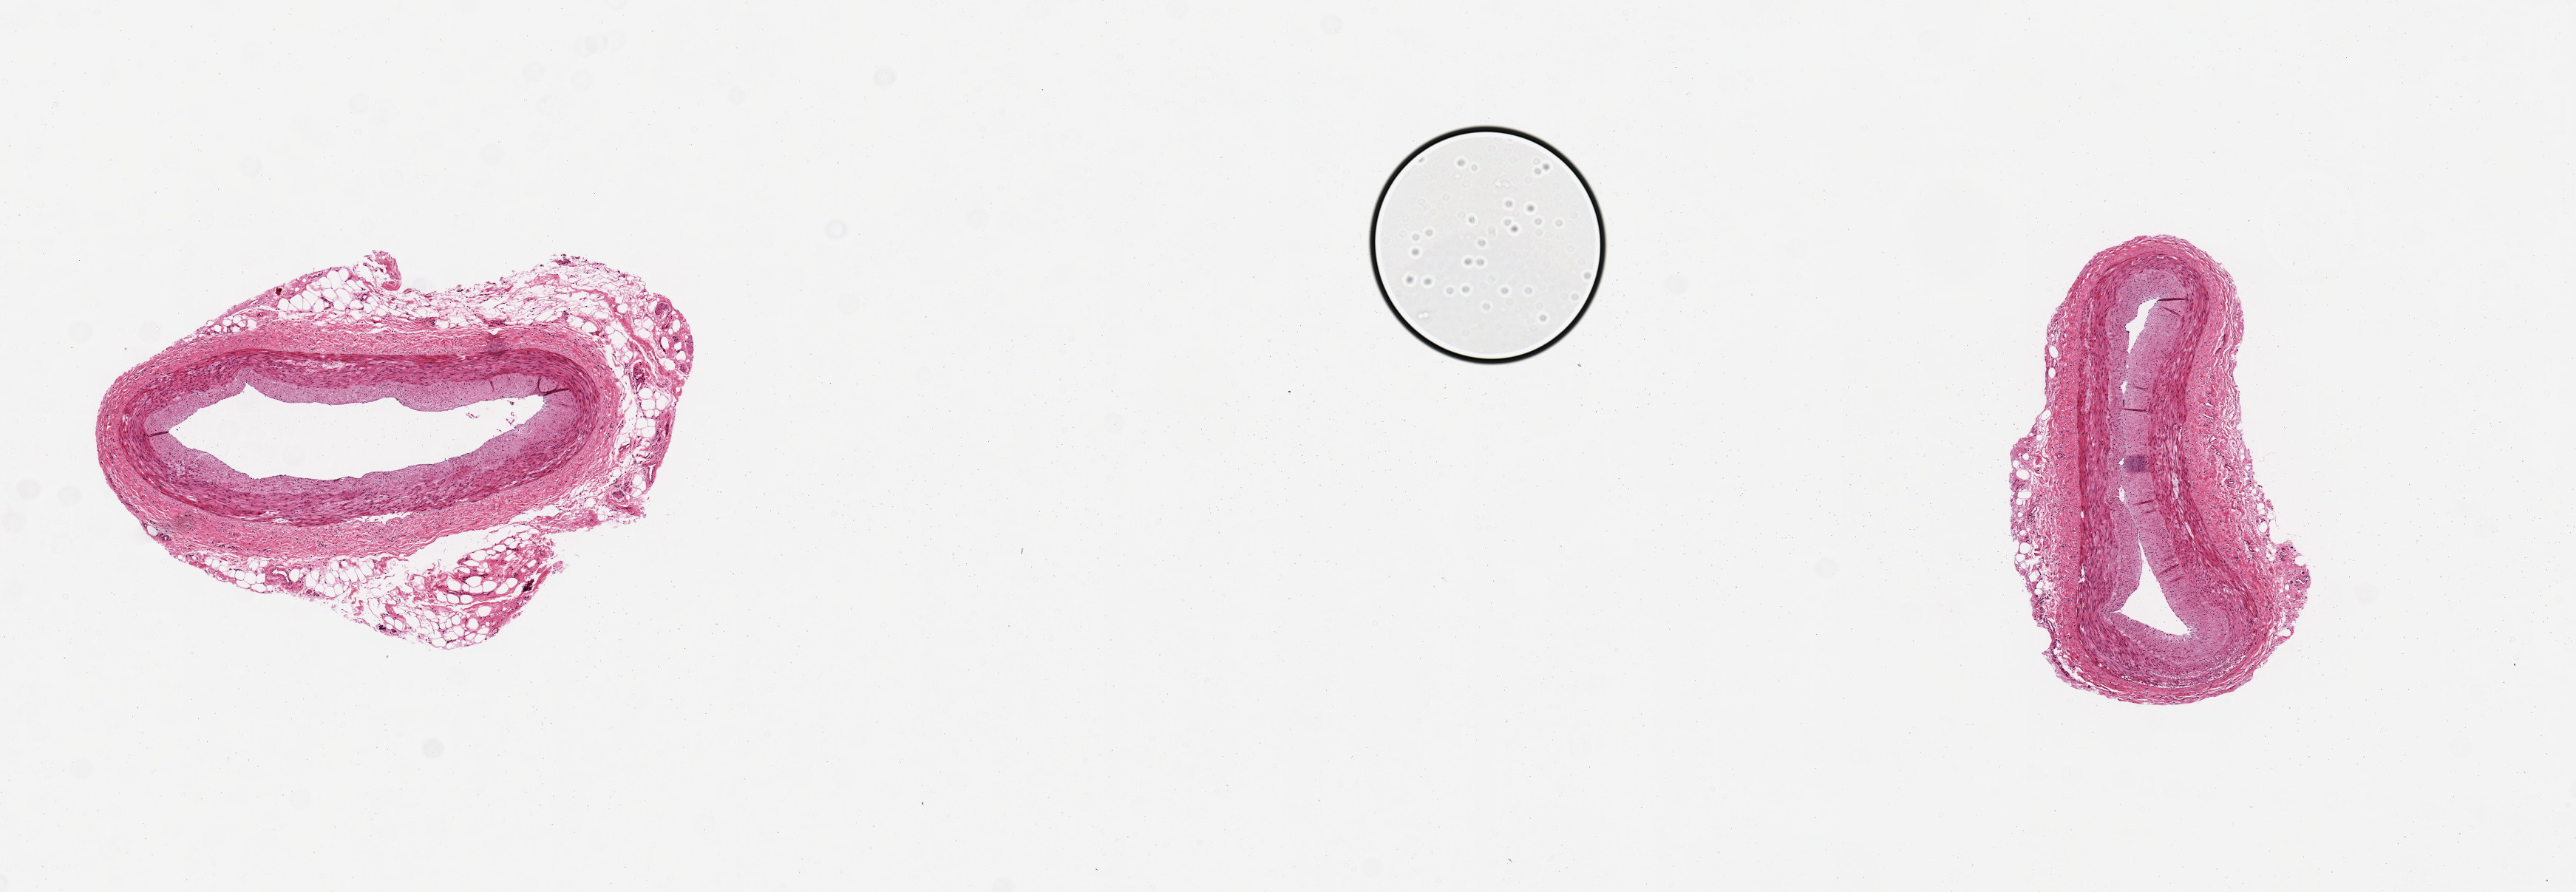
Digitized H&E-stained section, brightfield — whole scanned area (about 13.8 x 4.8 mm) shown as a low-resolution overview, PAXgene-fixed, paraffin-embedded tissue, section of coronary artery (target tissue), tissue donor sample. Male donor.
Pathologist's review note for this sample: Good clean specimen.